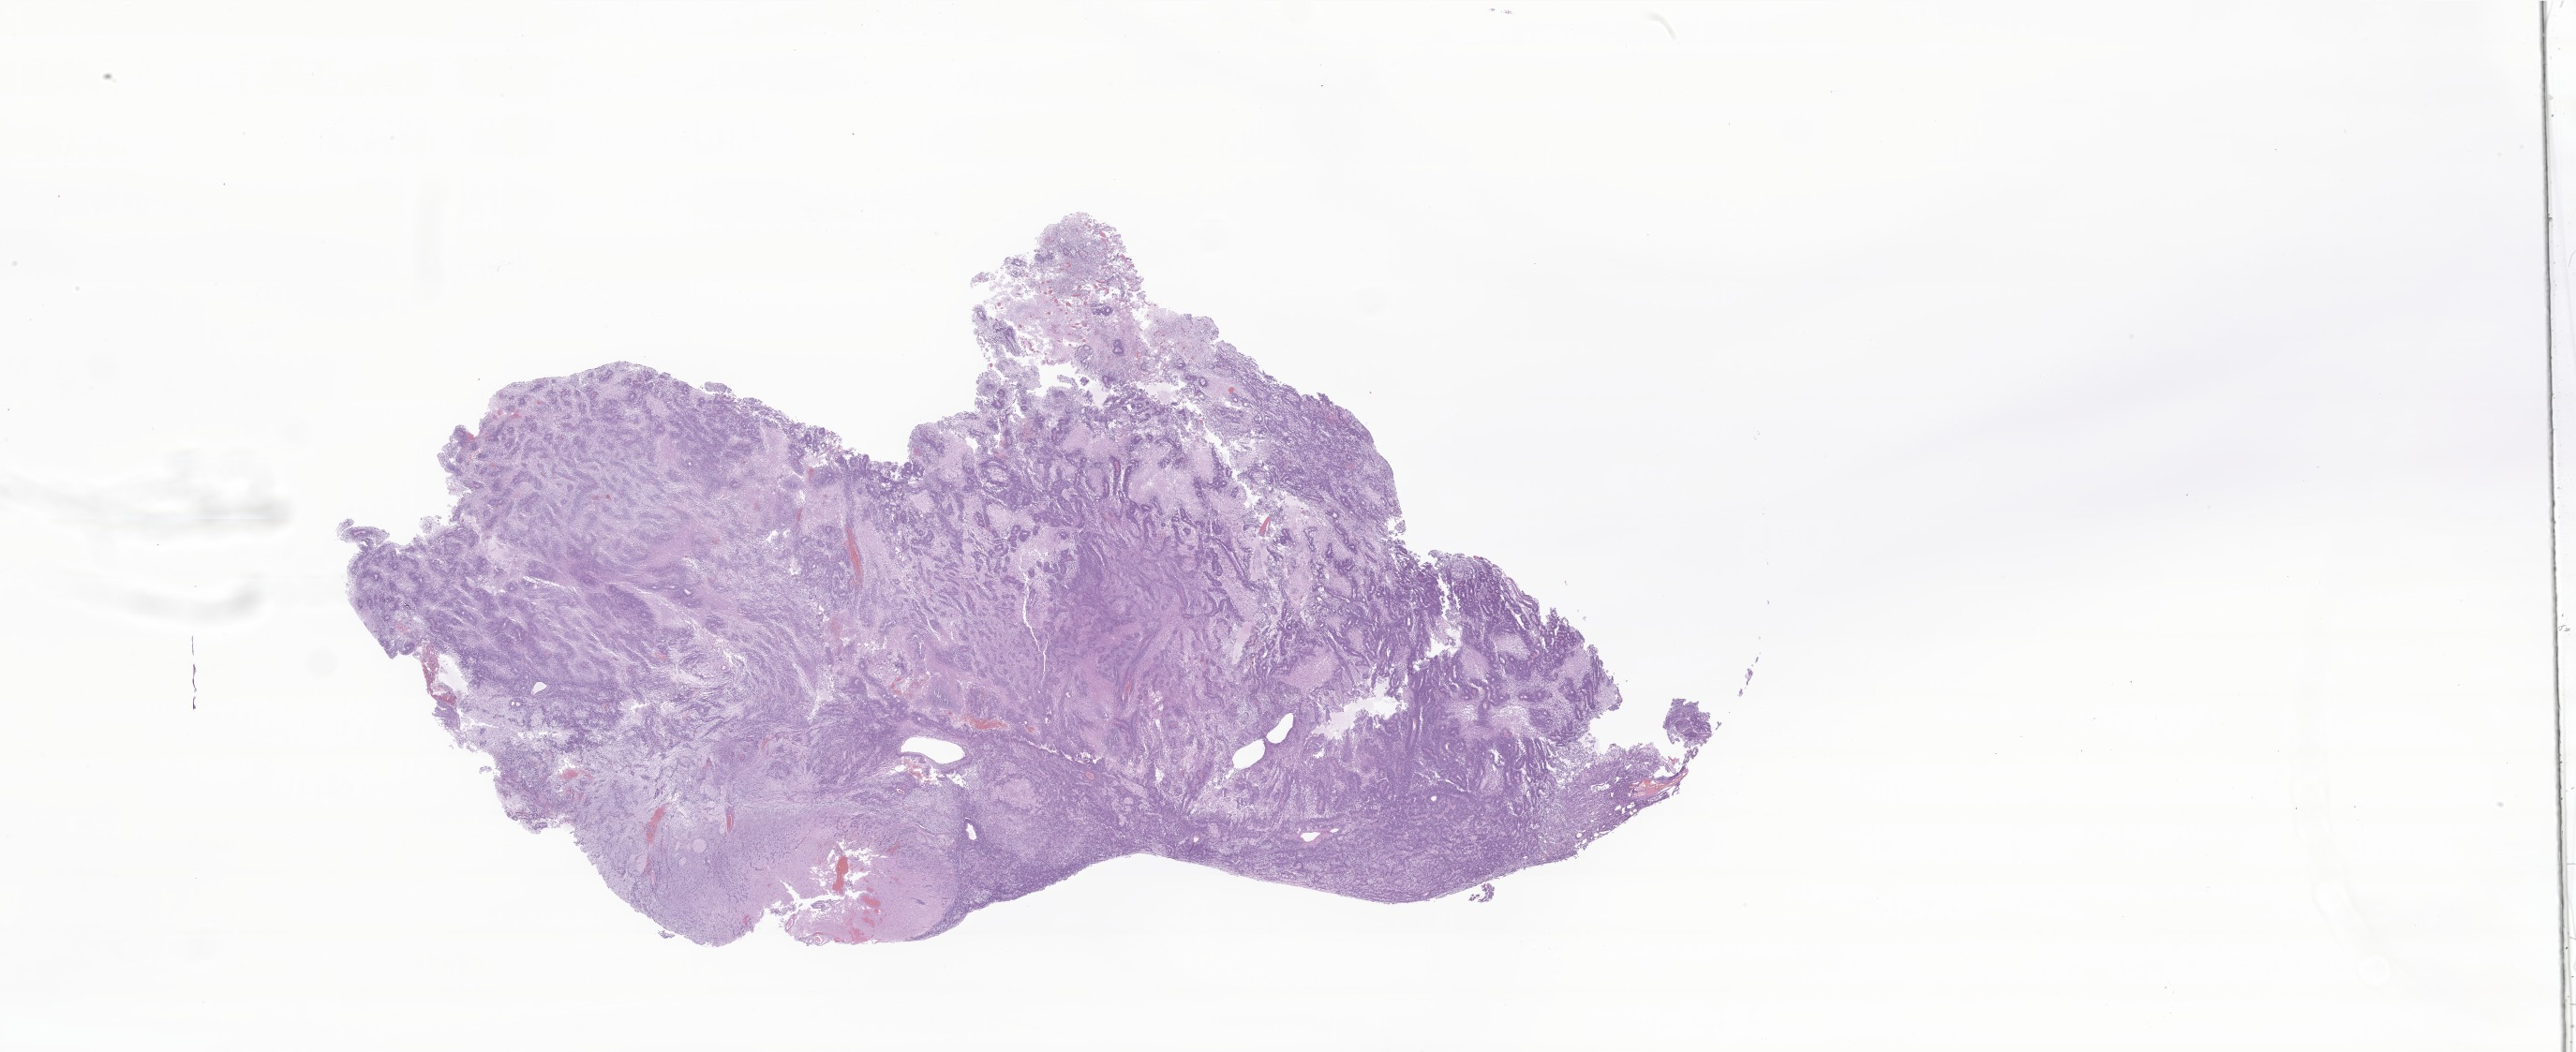
H&E whole-slide image of tumor tissue from the brain — low-resolution overview of the scanned area, about 46.4 x 18.9 mm. Formalin-fixed, paraffin-embedded (FFPE) tissue. Patient female; age 35 months (2 years 11 months).
Recorded diagnosis: CNS embryonal tumor, NOS.